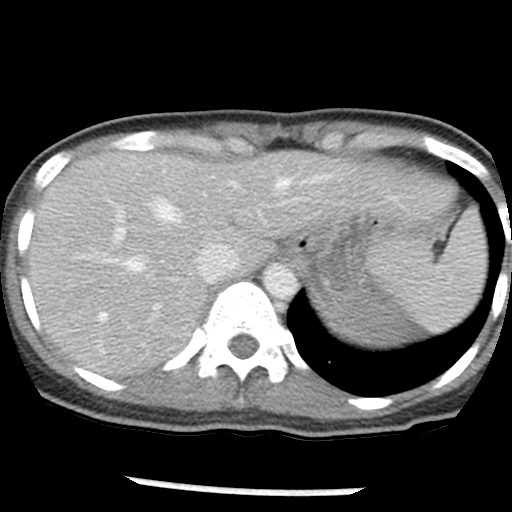
Contrast-enhanced abdominal CT, one axial slice; position 40 of 54 along the scan axis; reconstruction kernel STANDARD; 120 kVp; soft-tissue window (W 400 / L 40 HU); 5 mm slice thickness; 512 × 512 image matrix, field of view 240 × 240 mm. Patient: female, 33 years. Case-level facts recorded for this patient, not image findings: diagnosis: adrenocortical carcinoma; tumour side: left adrenal; tumour size at pathology: 11 cm; Ki-67 index: 20 %; stage (as recorded): 2.
Outlined on this slice (semi-automatic segmentation, software-assisted and operator-edited):
- mass: box from (x=325, y=287) to (x=421, y=346) px